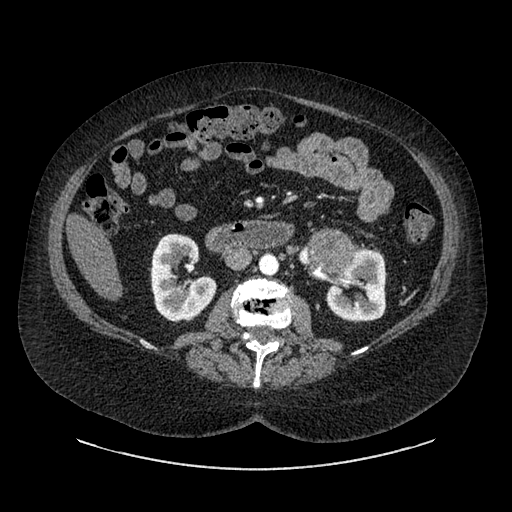
Contrast-enhanced abdominal CT, one axial slice. Position 492 of 769 along the scan axis. 120 kVp. Intravenous contrast given. Soft-tissue window (W 400 / L 40 HU). 0.62 mm slice thickness. 512 × 512 image matrix, field of view 460 × 460 mm. Female patient, age 61 years. Case-level facts recorded for this patient, not image findings: diagnosis: adrenocortical carcinoma; tumour side: left adrenal; tumour size at pathology: 13 cm; Ki-67 index: 79 %; stage (as recorded): 2.
Annotated regions visible in this slice (semi-automatically segmented with operator editing):
- mass: bounding box [x1, y1, x2, y2] px = [315, 235, 351, 271]